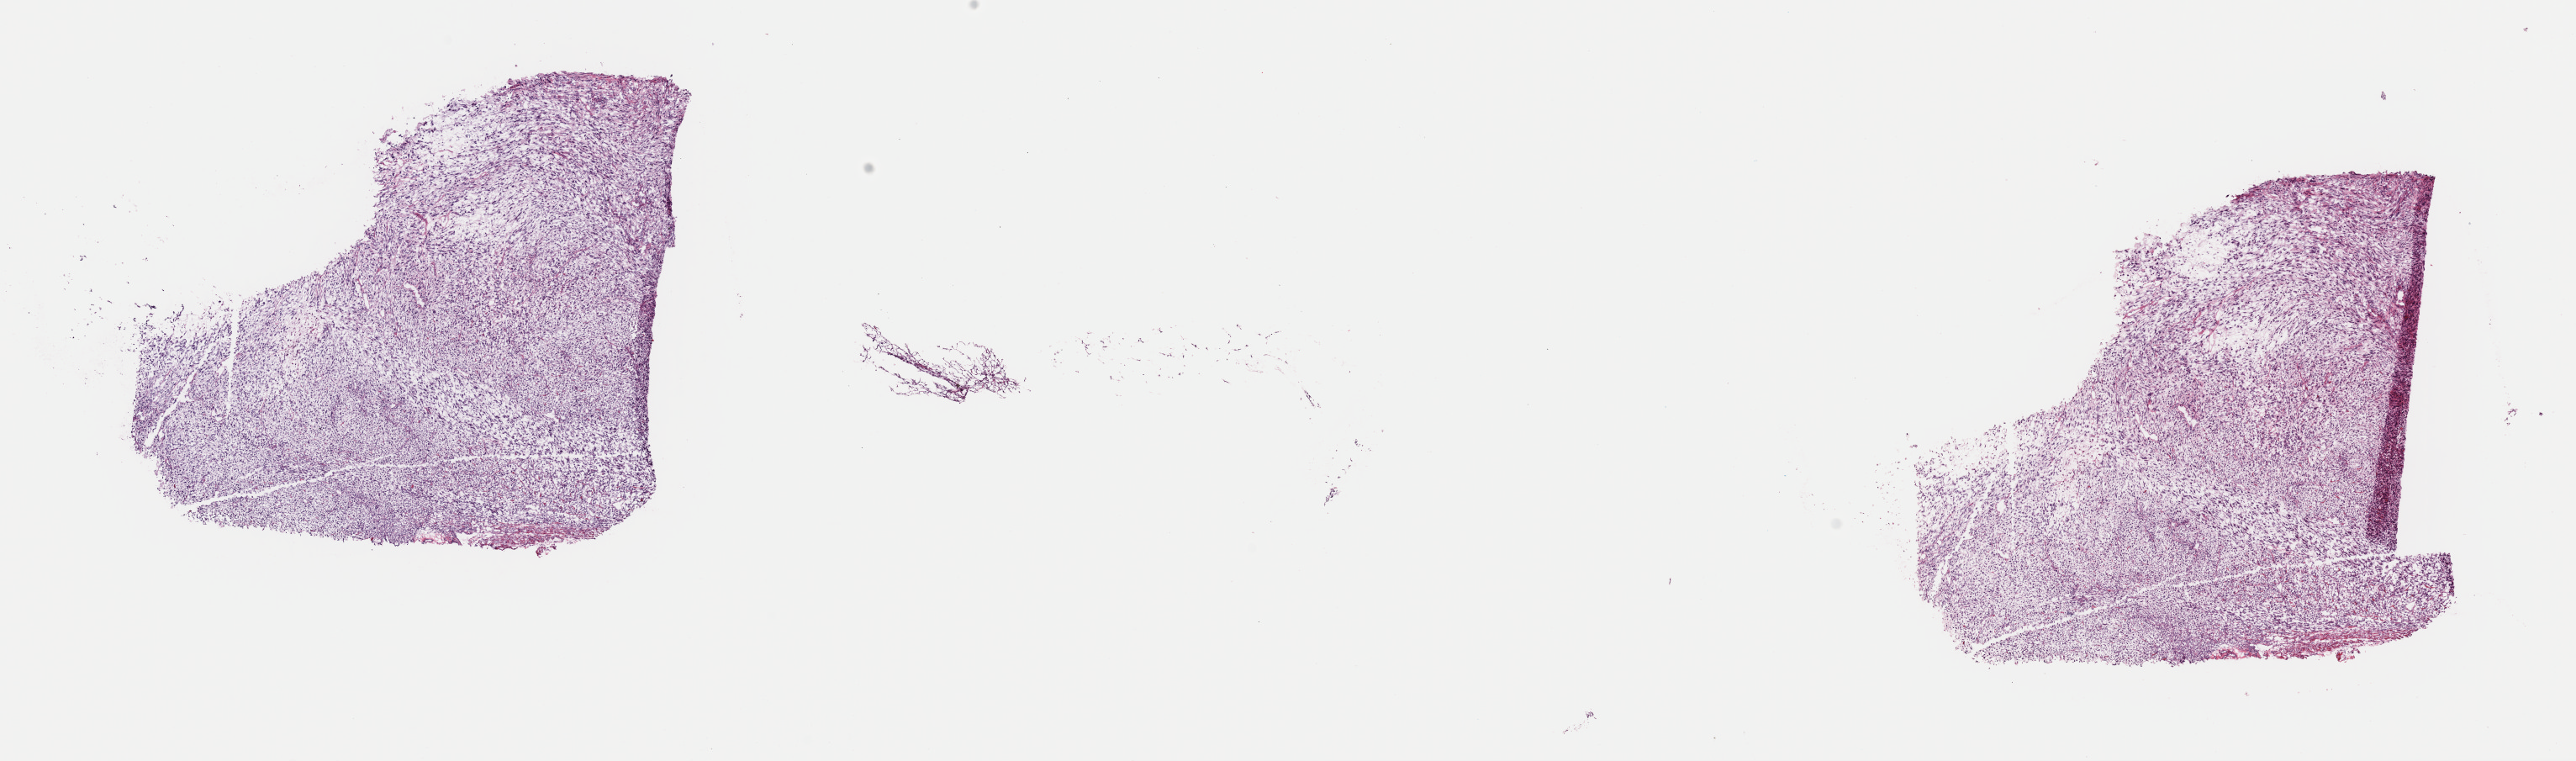
H&E-stained whole-slide image — a low-resolution overview of the entire scanned area, about 24.2 x 7.1 mm (acquisition: 40x scan); frozen section; connective, subcutaneous and other soft tissues, primary tumour sample. Patient sex: female. Slide review estimates, as recorded: tumour cells 95%, tumour nuclei 97%, normal cells 0%, stromal cells 5%, necrosis 0%. Infiltration values recorded for this section: lymphocyte infiltration 1%, monocyte infiltration 1%, neutrophil infiltration 0%.
Histologic diagnosis: Undifferentiated sarcoma (connective, subcutaneous and other soft tissues of lower limb and hip).